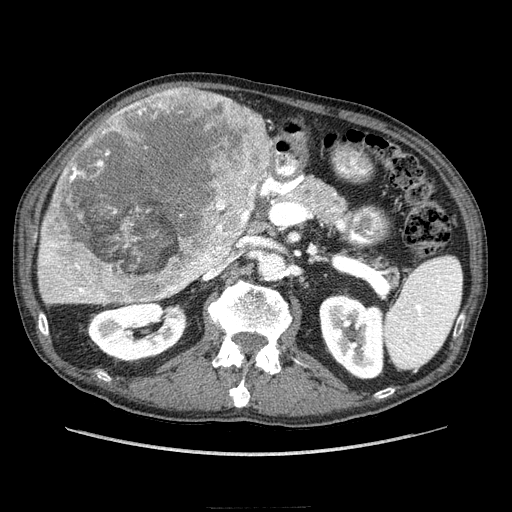
Contrast-enhanced abdominal CT (liver protocol), one axial slice. Slice 125 of 218 in the series (ordered by position). Soft-tissue window (W 400 / L 40 HU). 2.5 mm slice thickness. 512 × 512 image matrix, field of view 380 × 380 mm. From the clinical record (not read from this slice): diagnosis: hepatocellular carcinoma (patient treated with transarterial chemoembolisation; whether this scan precedes or follows treatment is not stated here); TNM stage (as recorded): Stage-IIIA; Child-Pugh class: A; tumour size: 20 cm.
Structures marked on this image (semi-automatic segmentation, software-assisted and operator-edited):
- liver parenchyma outside the tumour (the mass and vessels are separate outlines, so this box may not span the whole liver): bounding box (x1, y1, x2, y2) in pixels: (38, 121, 270, 304)
- mass: (42, 80, 276, 304)
- liver vessels: (42, 261, 100, 300)